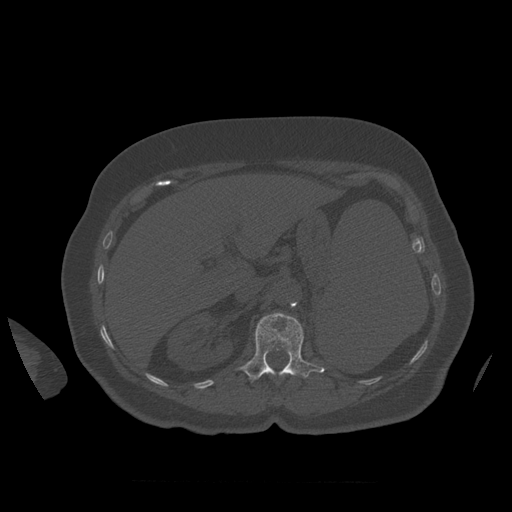
CT including the spine, one axial slice. Position 281 of 399 along the scan axis. Reconstruction kernel STANDARD. 120 kVp. Bone window (W 1800 / L 400 HU). 1.25 mm slice thickness. 512 × 512 image matrix, field of view 404 × 404 mm. Patient age 81 years. From the clinical record (not read from this slice): primary cancer: renal; vertebrae with lytic lesions (as recorded): L1.
Annotated regions visible in this slice (semi-automatically segmented with operator editing):
- L1 vertebra: box from (x=239, y=313) to (x=325, y=382) px